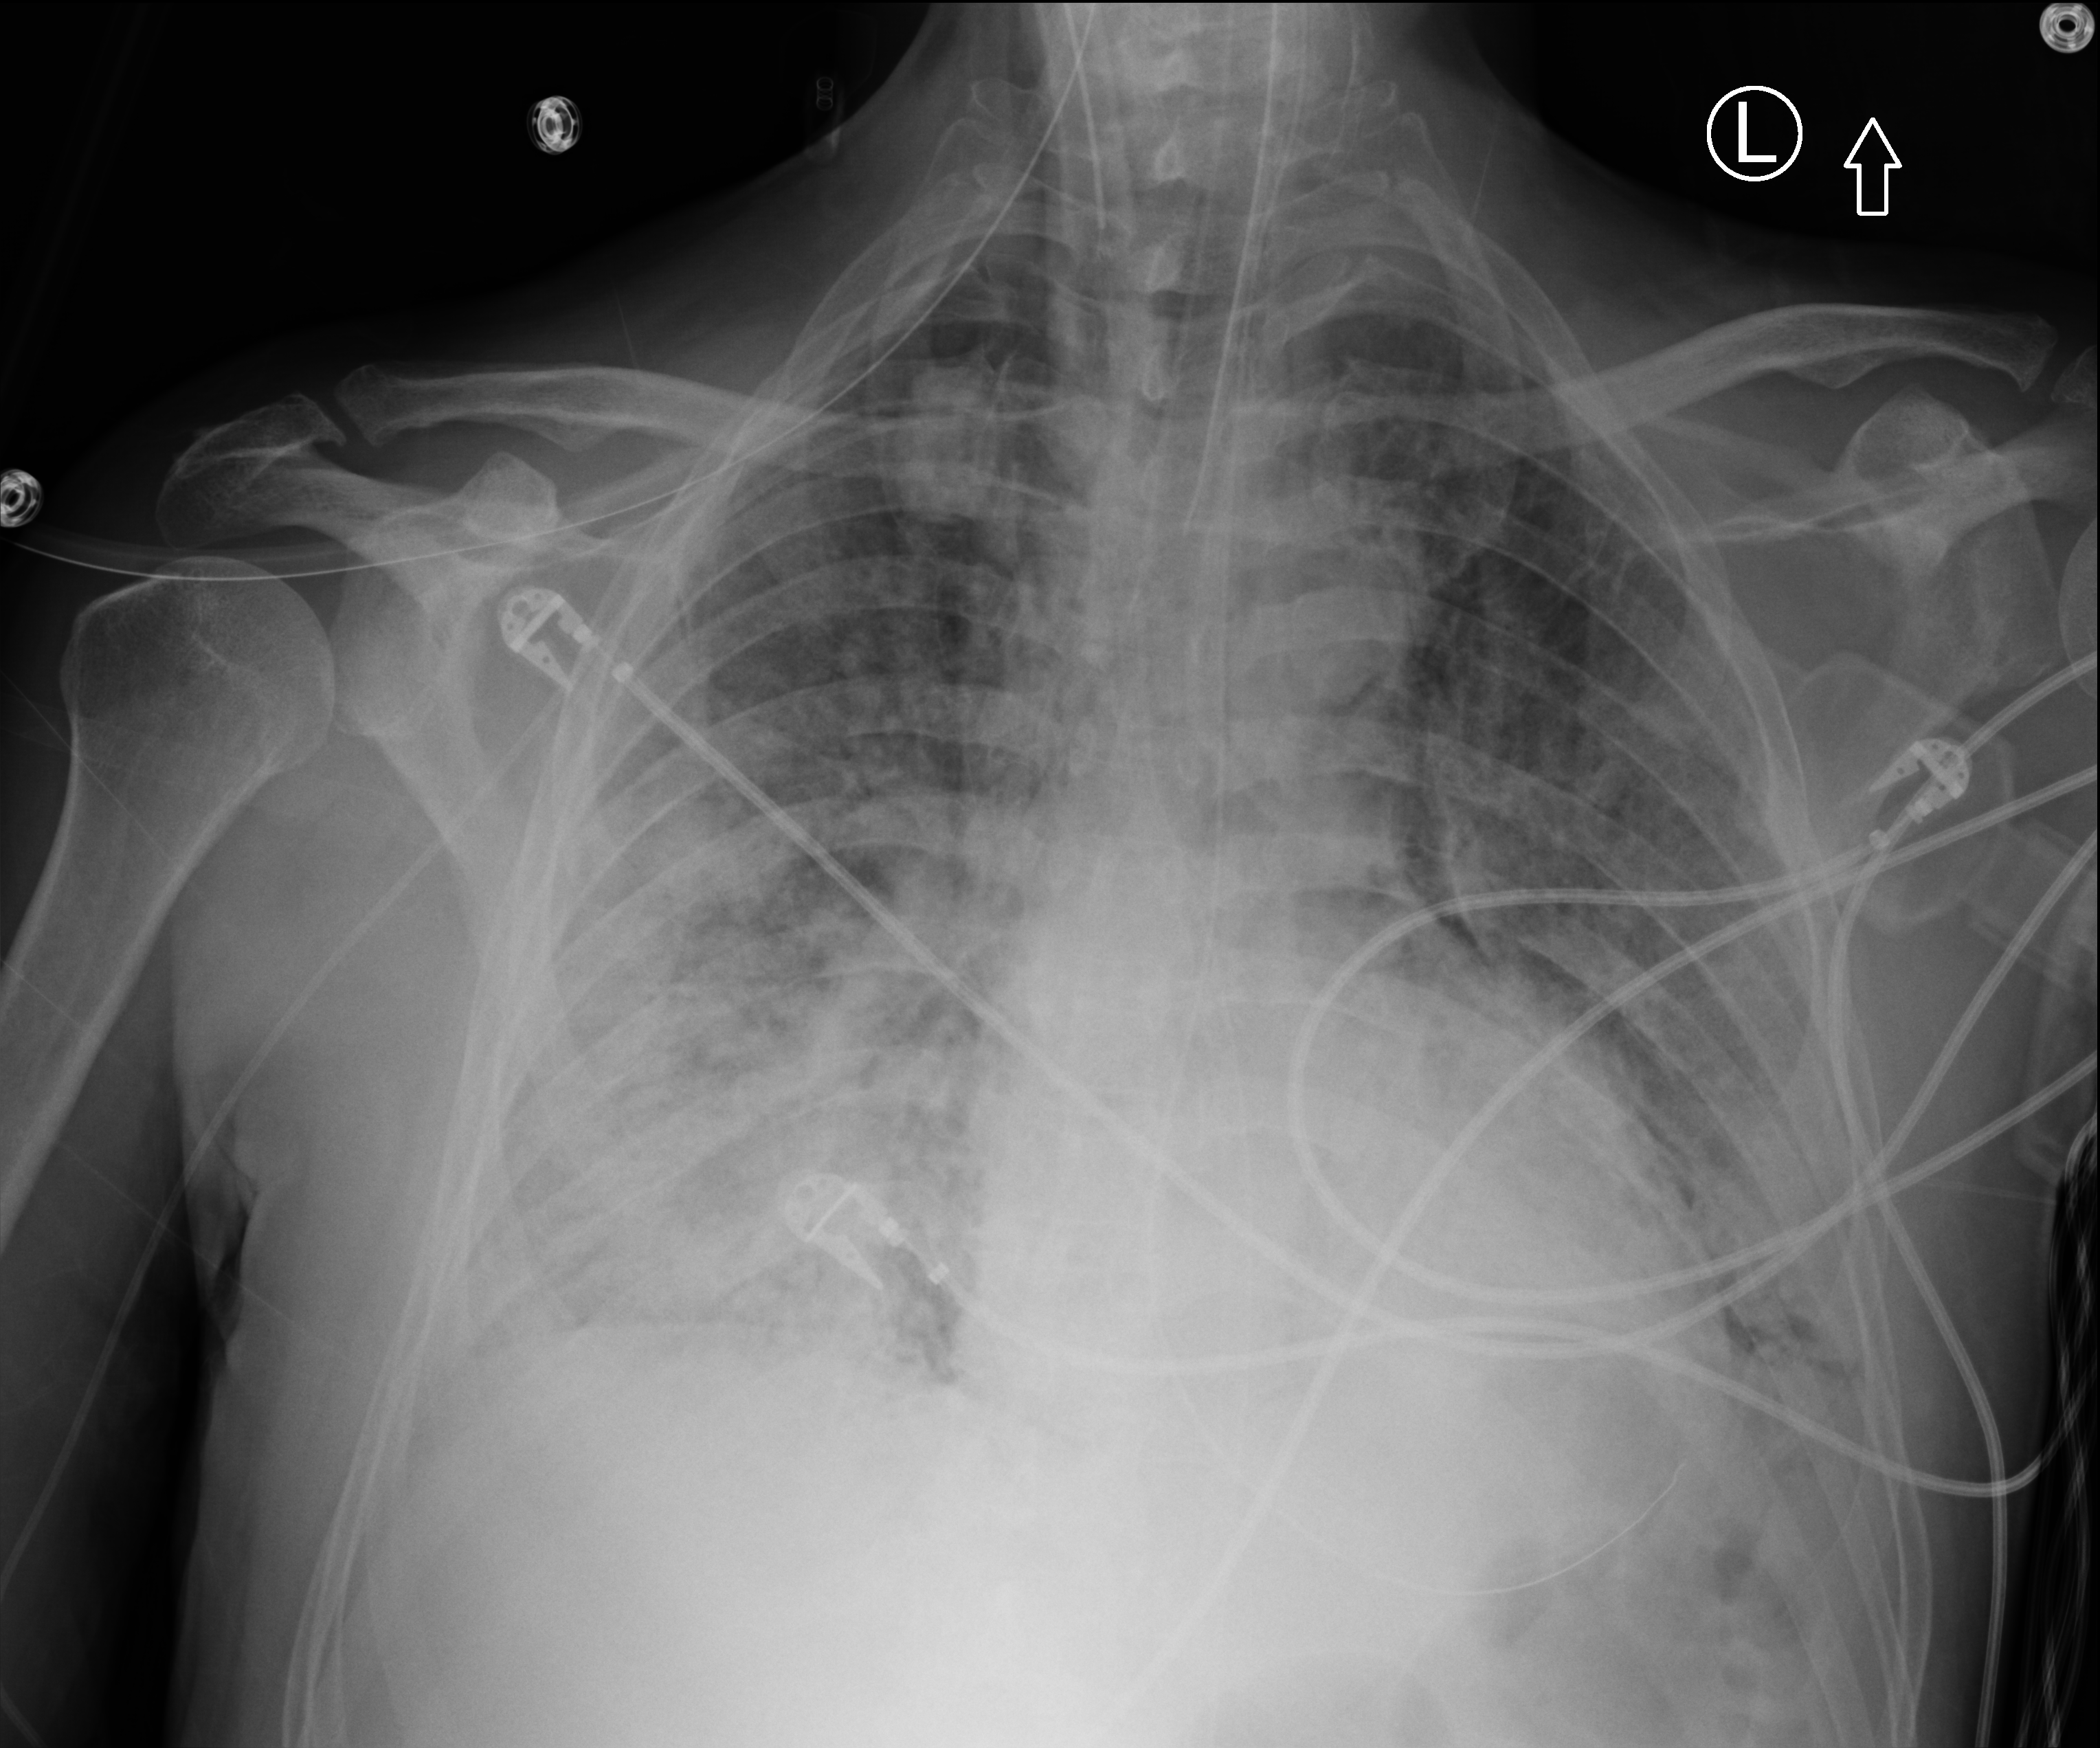
Chest X-ray (portable); anteroposterior (AP) projection. Male patient hospitalised with COVID-19, age 60–74 years.
Hospital-stay facts (about this admission, not read from this image; timing relative to this image not recorded): smoking status (admission record): never; admitted to intensive care during this hospital stay: yes; mechanically ventilated during this hospital stay: yes.